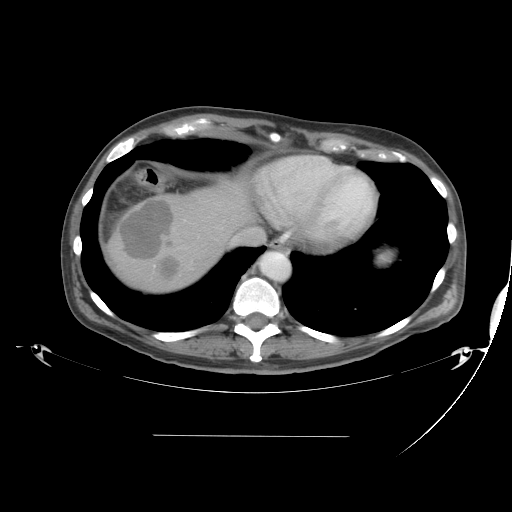
Contrast-enhanced abdominal CT, one axial slice. Position 38 of 48 along the scan axis. Reconstruction kernel STANDARD. 120 kVp. Intravenous contrast given. Soft-tissue window (W 400 / L 40 HU). 5 mm slice thickness. 512 × 512 image matrix, field of view 486 × 486 mm. Male patient, age 65 years. Case-level facts recorded for this patient, not image findings: diagnosis: colorectal cancer liver metastases, imaged before liver resection; multiple liver metastases: yes; largest metastasis: 11 cm; disease in both lobes: yes.
Outlined on this slice (outlined manually by an expert reader):
- hepatic veins: bounding box <173,226,224,249> (left, top, right, bottom; pixels)
- liver: <109,183,253,294>
- planned liver remnant (the part of the liver to remain after resection): <198,182,254,229>
- portal vein (with intrahepatic branches): <213,202,226,223>
- liver metastasis: <157,258,180,278>
- liver metastasis: <115,200,173,260>